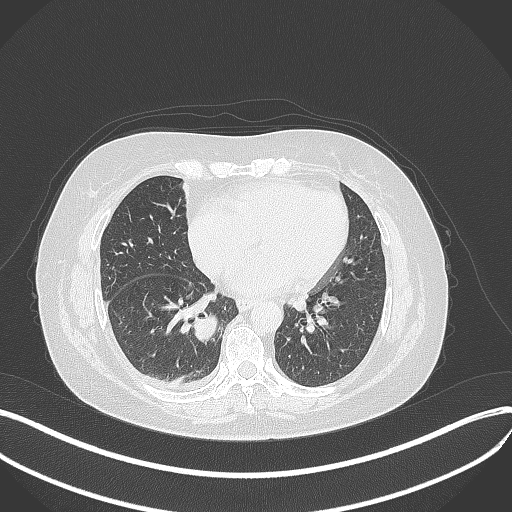
Chest CT, one axial slice; slice 143 of 381 in the series (ordered by position); reconstruction kernel B70f; 120 kVp; lung window (W 1500 / L -600 HU); 1 mm slice thickness; 512 × 512 image matrix, field of view 400 × 400 mm. Female patient, age 56 years. From the clinical record (not read from this slice): clinical TNM (as recorded): T2b N1 M0.
Annotated regions visible in this slice (rectangle marked by the reading radiologist):
- lung tumour (recorded histology: small cell carcinoma): bounding box <194,311,220,350> (left, top, right, bottom; pixels)